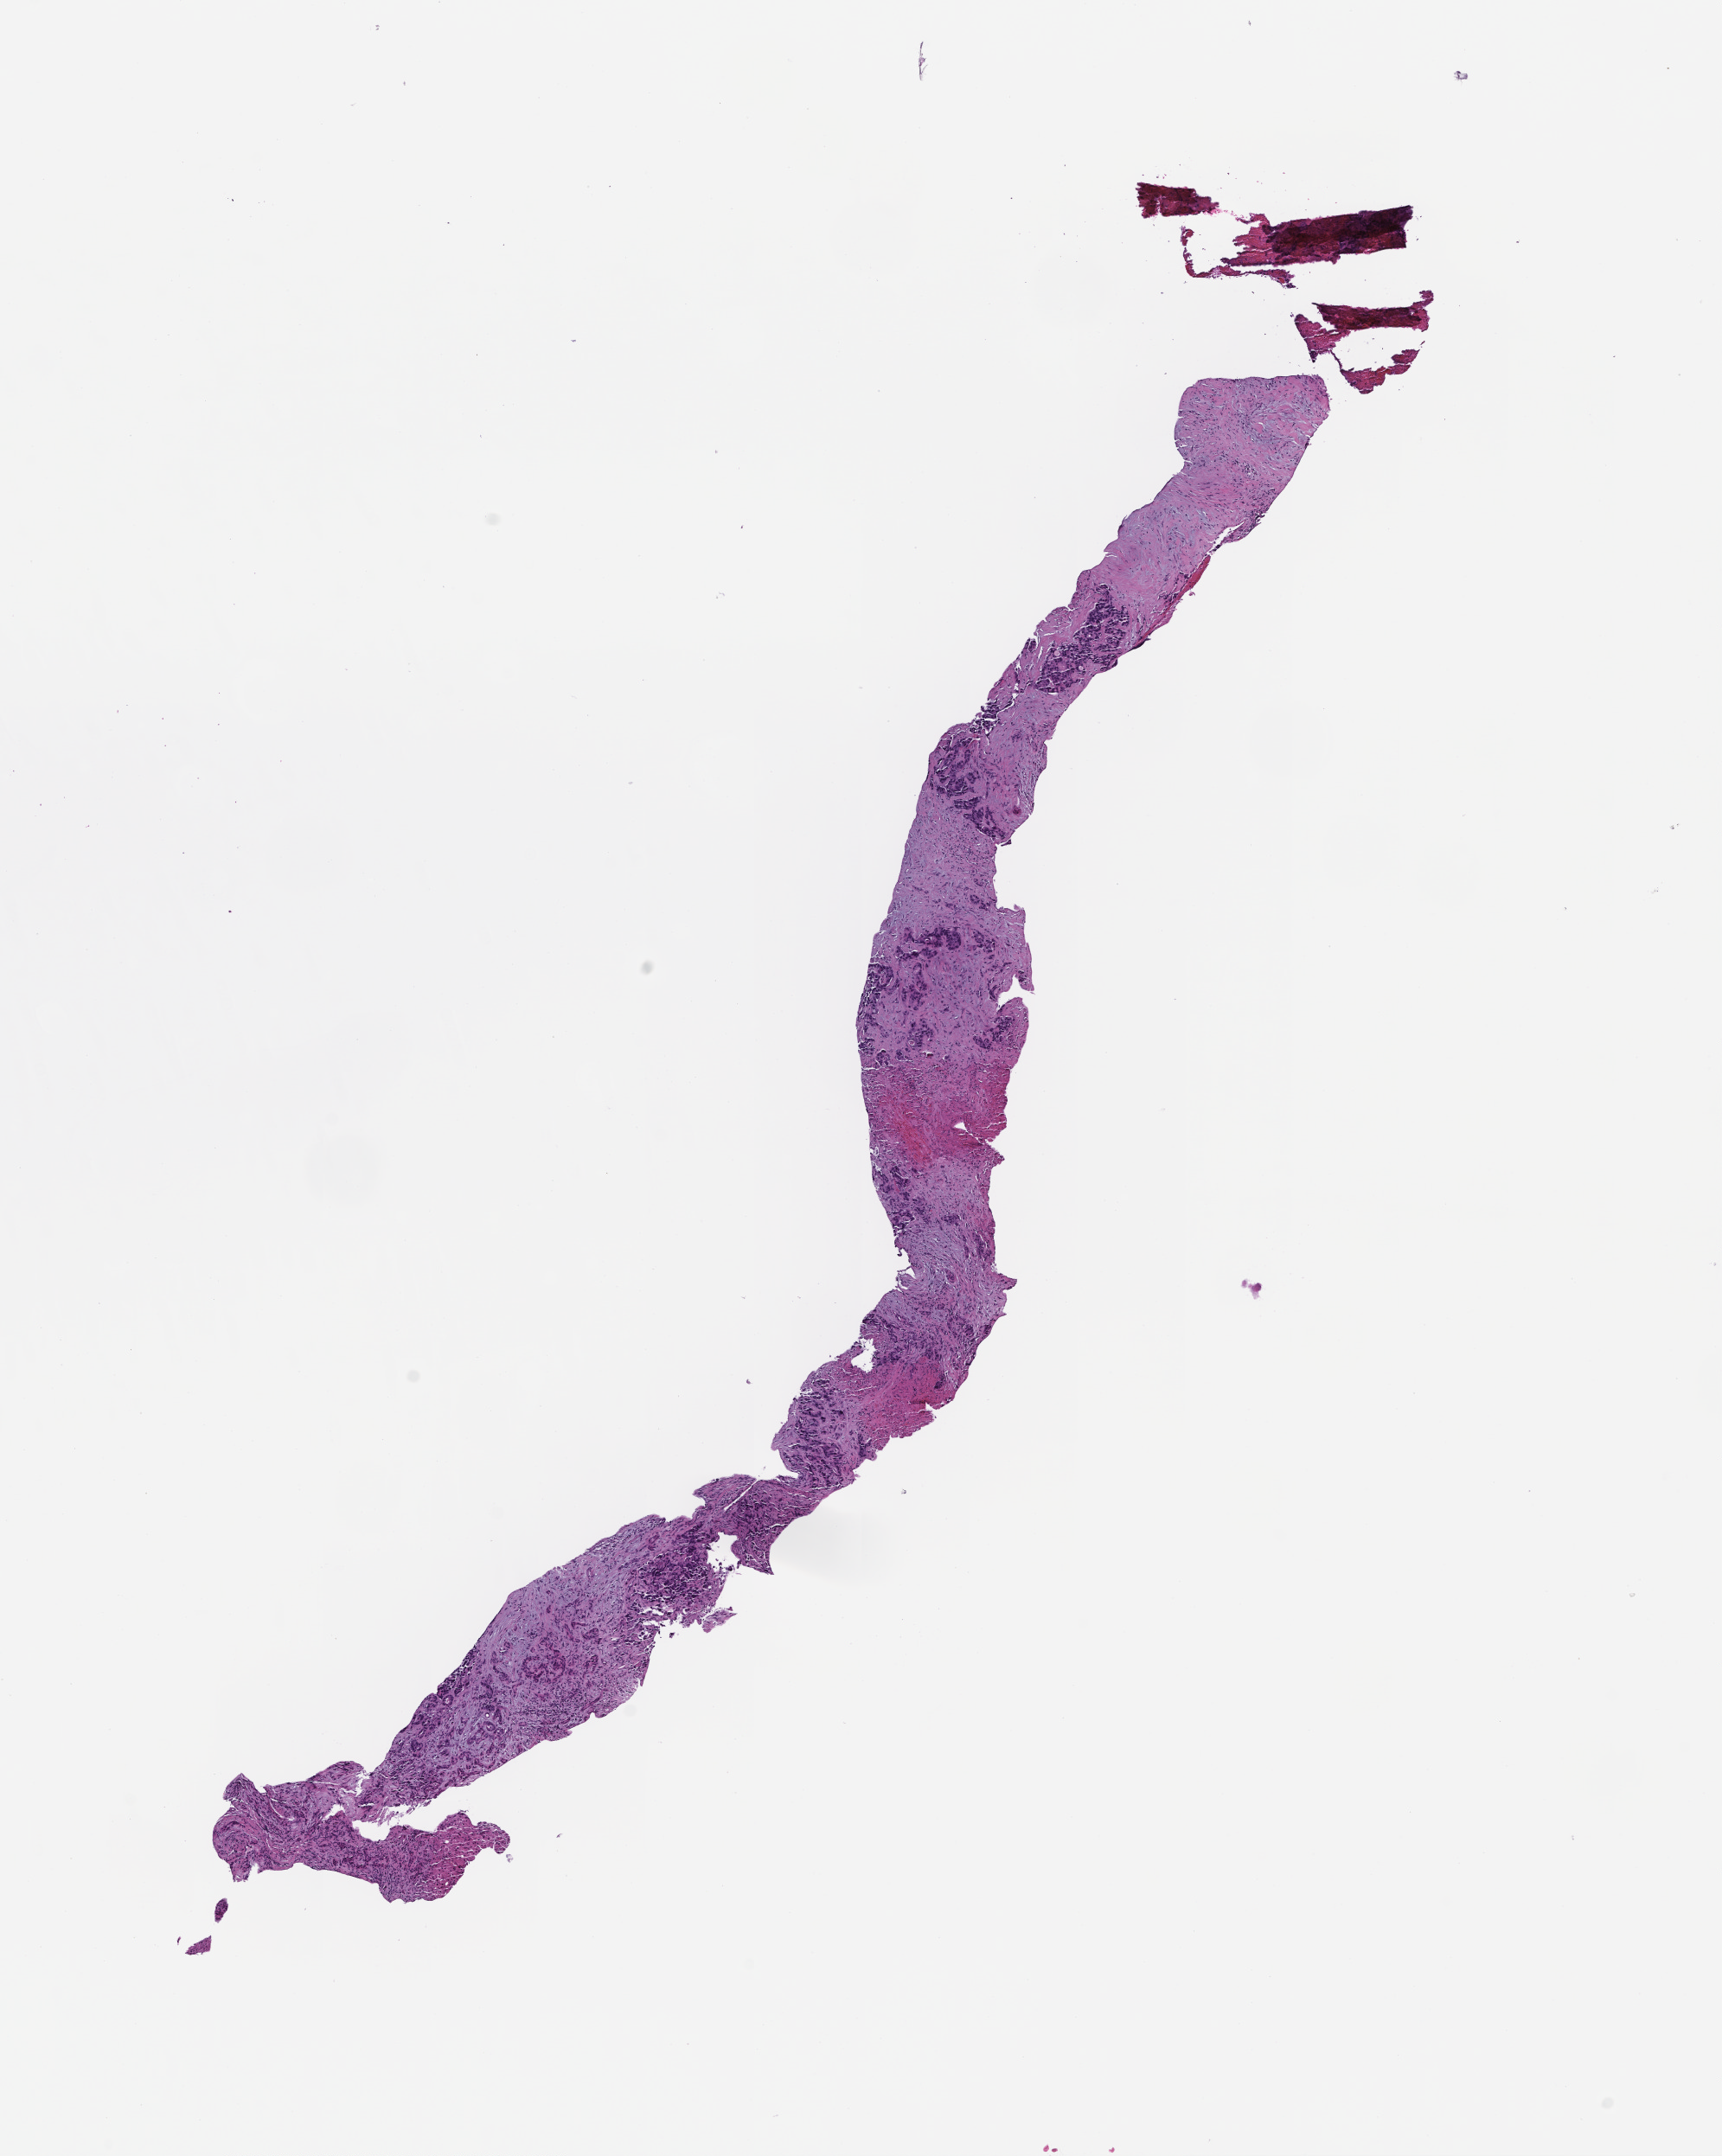
Digitized hematoxylin and eosin (H&E)-stained section, shown as a low-resolution overview of the whole scanned area (about 8.0 x 10.1 mm), FFPE section, specimen time point: collected at disease progression. Patient: male.
This section: metastasis (sampled organ not recorded). Patient diagnosis (primary): Colorectal Carcinoma.